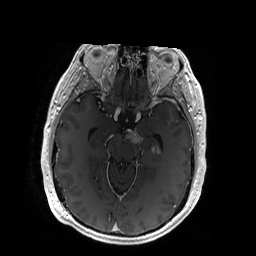
Brain MRI from a brain-tumour surgery series, one axial slice; position 115 of 192 along the scan axis; T1-weighted post-contrast; 1 mm slice thickness; 256 × 256 image matrix, field of view 256 × 256 mm. From the clinical record (not read from this slice): histopathology: Glioblastoma; WHO grade: 4; IDH mutation: no.
Annotated regions visible in this slice (expert manual segmentation):
- tumour: bounding box <126,129,160,155> (left, top, right, bottom; pixels)